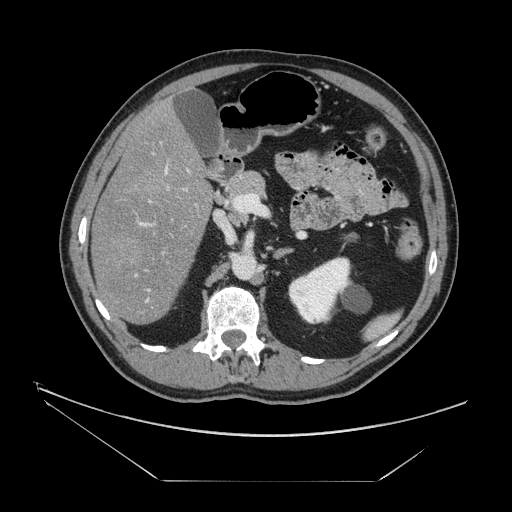
Contrast-enhanced abdominal CT, one axial slice; slice 77 of 161 in the series (ordered by position); reconstruction kernel STANDARD; soft-tissue window (W 400 / L 40 HU); 2.5 mm slice thickness; 512 × 512 image matrix, field of view 440 × 440 mm. Male patient, age 65 years. From the clinical record (not read from this slice): diagnosis: colorectal cancer liver metastases, imaged before liver resection; multiple liver metastases: yes; largest metastasis: 4.2 cm; disease in both lobes: yes.
Annotated regions visible in this slice (manually delineated by an expert):
- hepatic veins: bounding box (x1, y1, x2, y2) in pixels: (134, 163, 169, 303)
- liver: (92, 104, 213, 324)
- planned liver remnant (the part of the liver to remain after resection): (119, 116, 202, 321)
- portal vein (with intrahepatic branches): (111, 153, 202, 314)